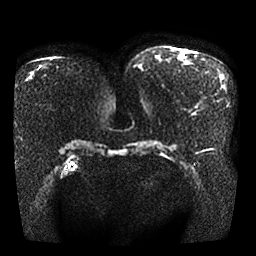
Breast MRI, one axial slice. Position 4 of 25 along the scan axis. Diffusion-weighted series; image 2 of 4 stored at this slice position (different b-values; order by instance number). 1.5 T. 256 × 256 image matrix, field of view 370 × 370 mm. Female patient.
Annotated regions visible in this slice (expert manual segmentation):
- tumour on diffusion-weighted imaging: box from (x=198, y=101) to (x=207, y=111) px